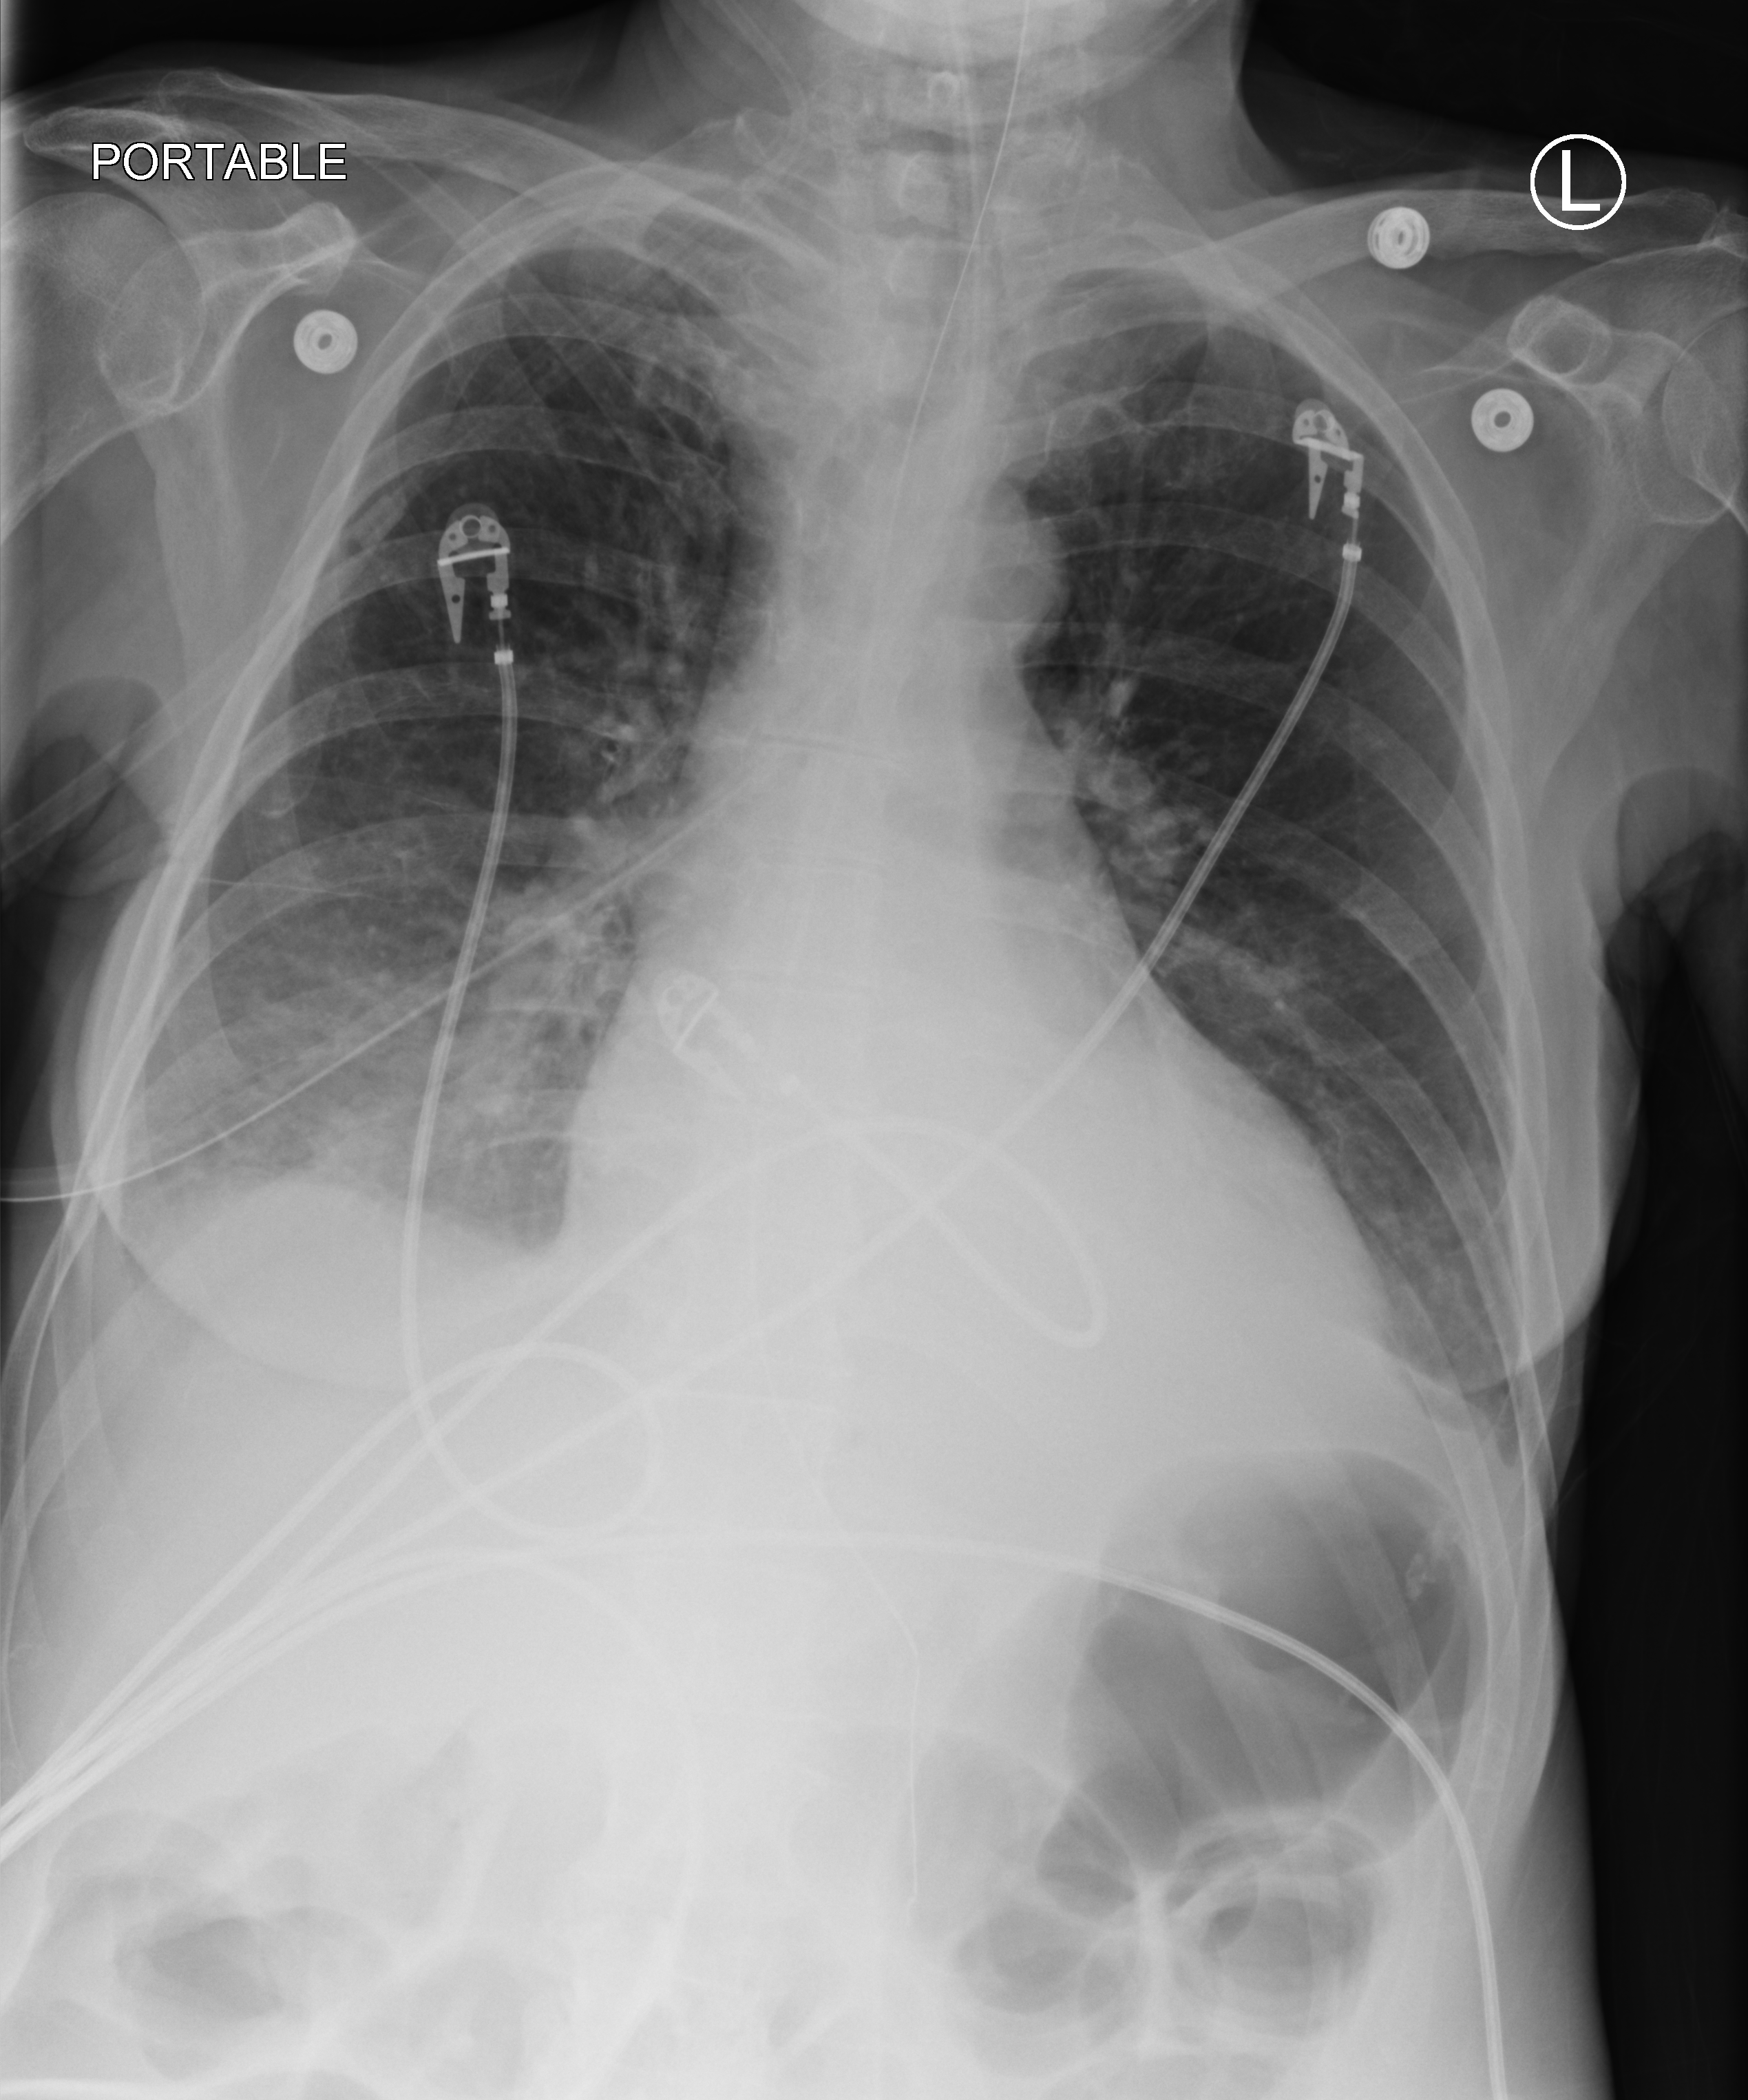
Bedside chest radiograph (computed radiography). Female patient hospitalised with COVID-19, age 60–74 years.
Admission-level facts for this patient (not findings on this image; timing relative to this image not recorded): mechanically ventilated during this hospital stay: yes.